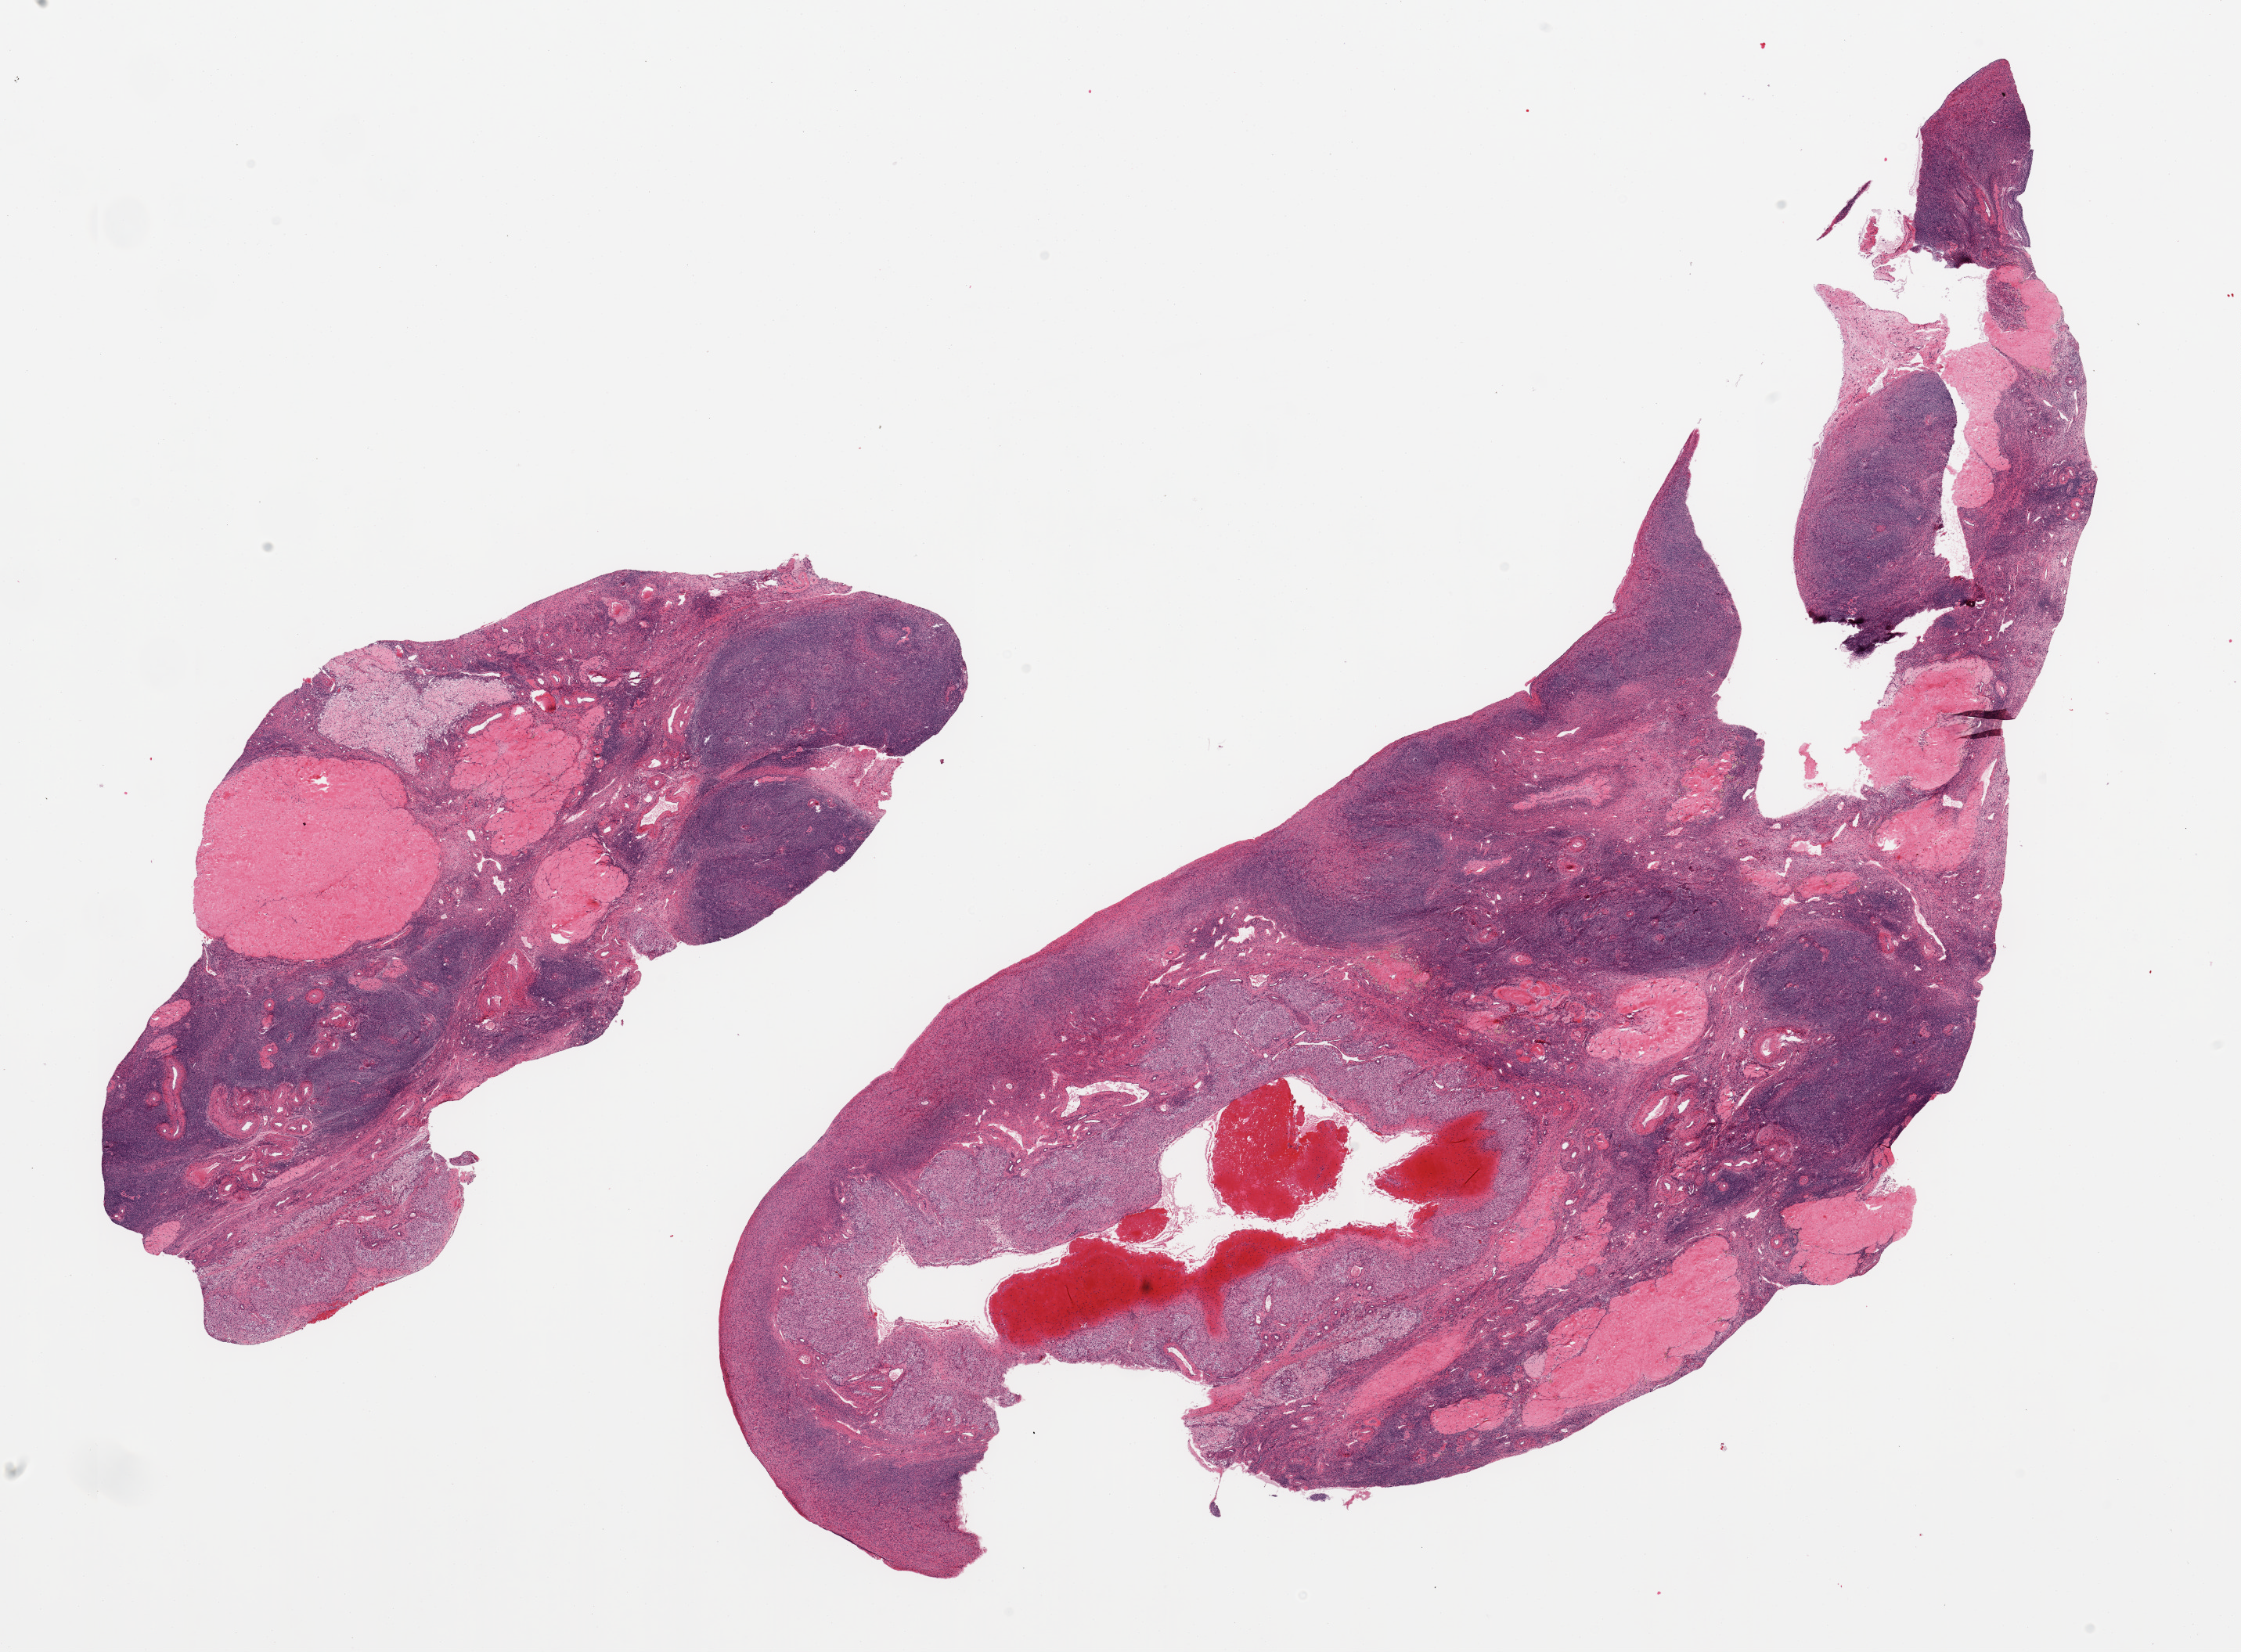
Whole-slide image, haematoxylin and eosin stain, whole scanned area (about 22.6 x 16.7 mm) shown as a low-resolution overview. PAXgene-fixed, paraffin-embedded tissue. Sampled site (target tissue): ovary. Tissue donor sample. Donor: female.
• pathologist's review note for this sample: 2 pieces; corpora albicantia and corpus luteum